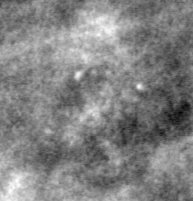
Crop from a digitized film mammogram around one marked abnormality, left breast, MLO view, BI-RADS breast density category 3 (scale 1–4).
Finding: calcifications, morphology pleomorphic, distribution clustered; BI-RADS assessment category 4; subtlety rating 2 on a 1 (subtle) to 5 (obvious) scale; pathology result (as recorded, not read from the image): benign.